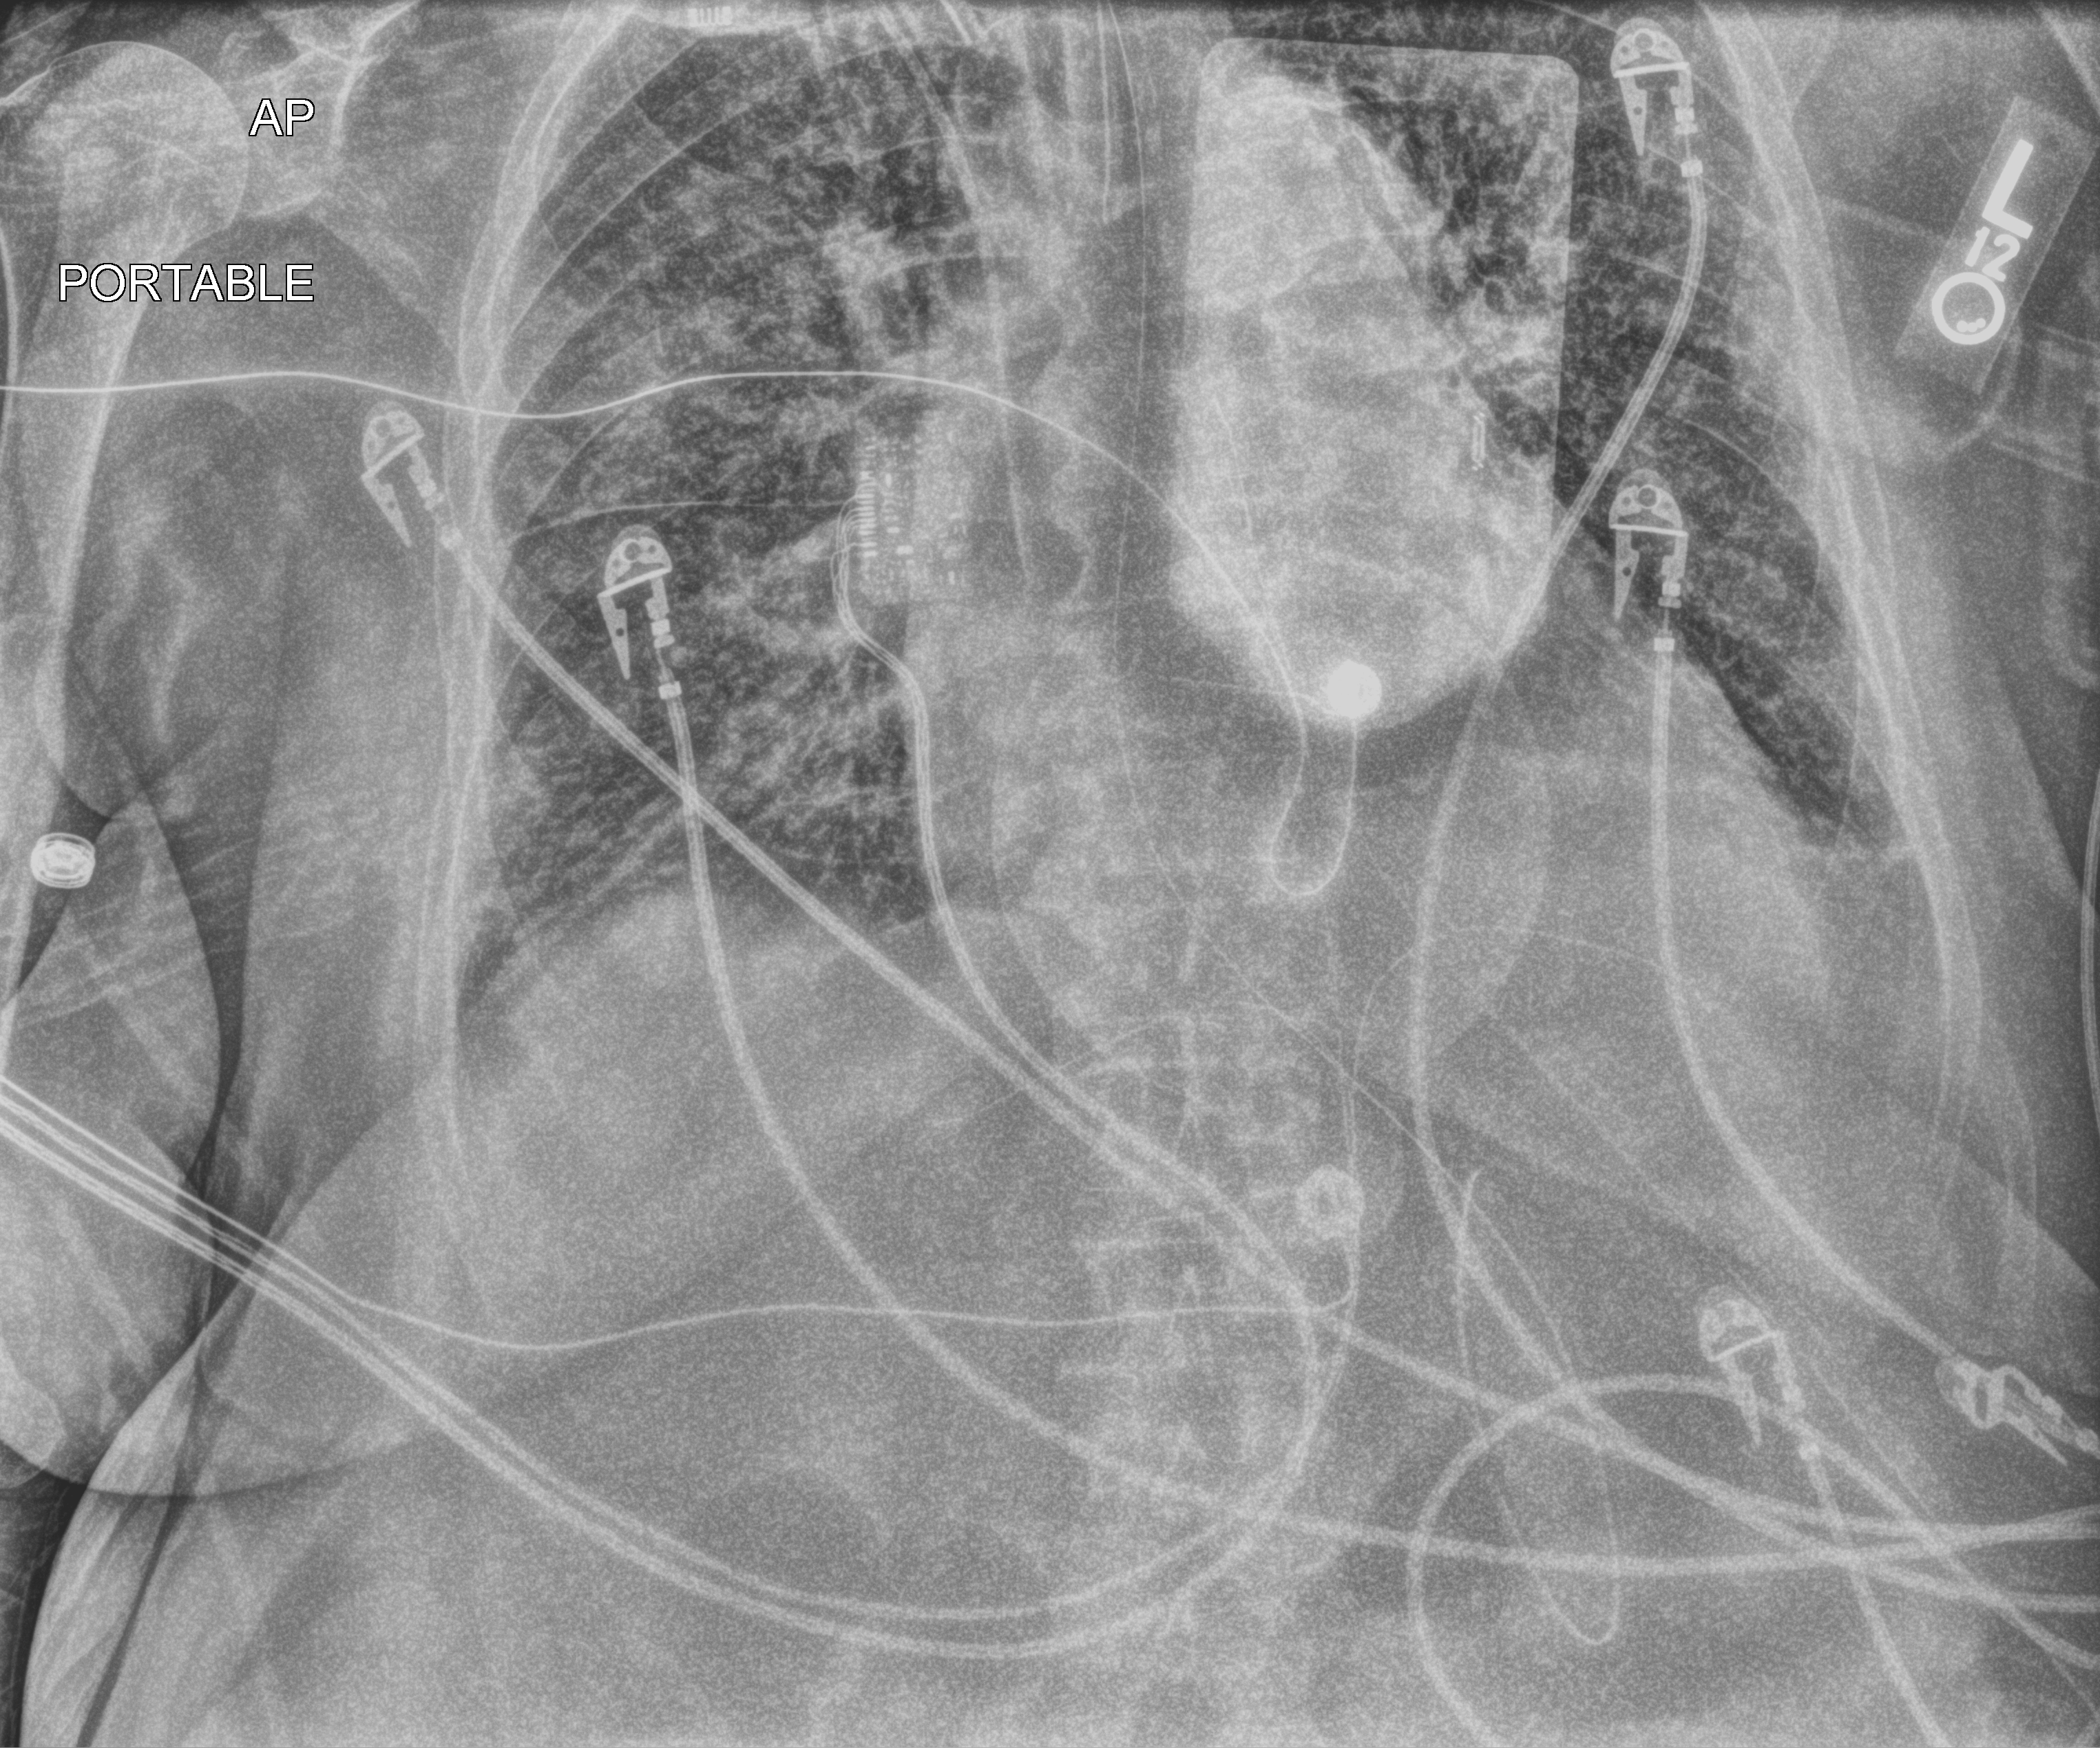
Bedside chest radiograph (computed radiography), anteroposterior (AP) projection. Female patient hospitalised with COVID-19, age 75–90 years.
From the hospital-stay record, not from the radiograph (when in the stay this image was taken is not recorded): other chronic lung disease (admission record): no; admitted to intensive care during this hospital stay: yes.